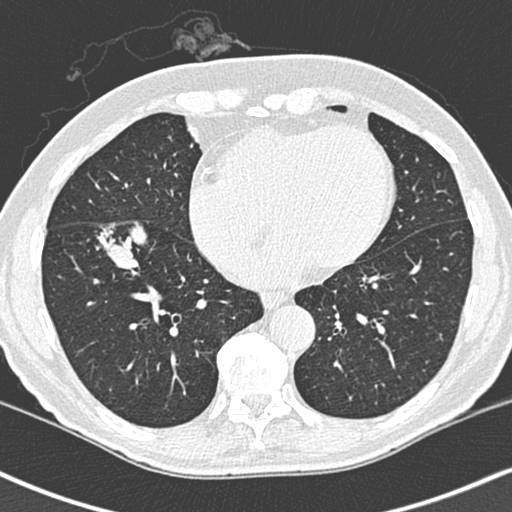
Low-dose screening chest CT, one axial slice; slice 101 of 248 in the series (ordered by position); 120 kVp; lung window (W 1500 / L -600 HU); 1.3 mm slice thickness; 512 × 512 image matrix.
Annotated regions visible in this slice (expert manual segmentation):
- lesion 1 (tumor, lower lobe of right lung): bounding box [x1, y1, x2, y2] px = [97, 183, 147, 230]